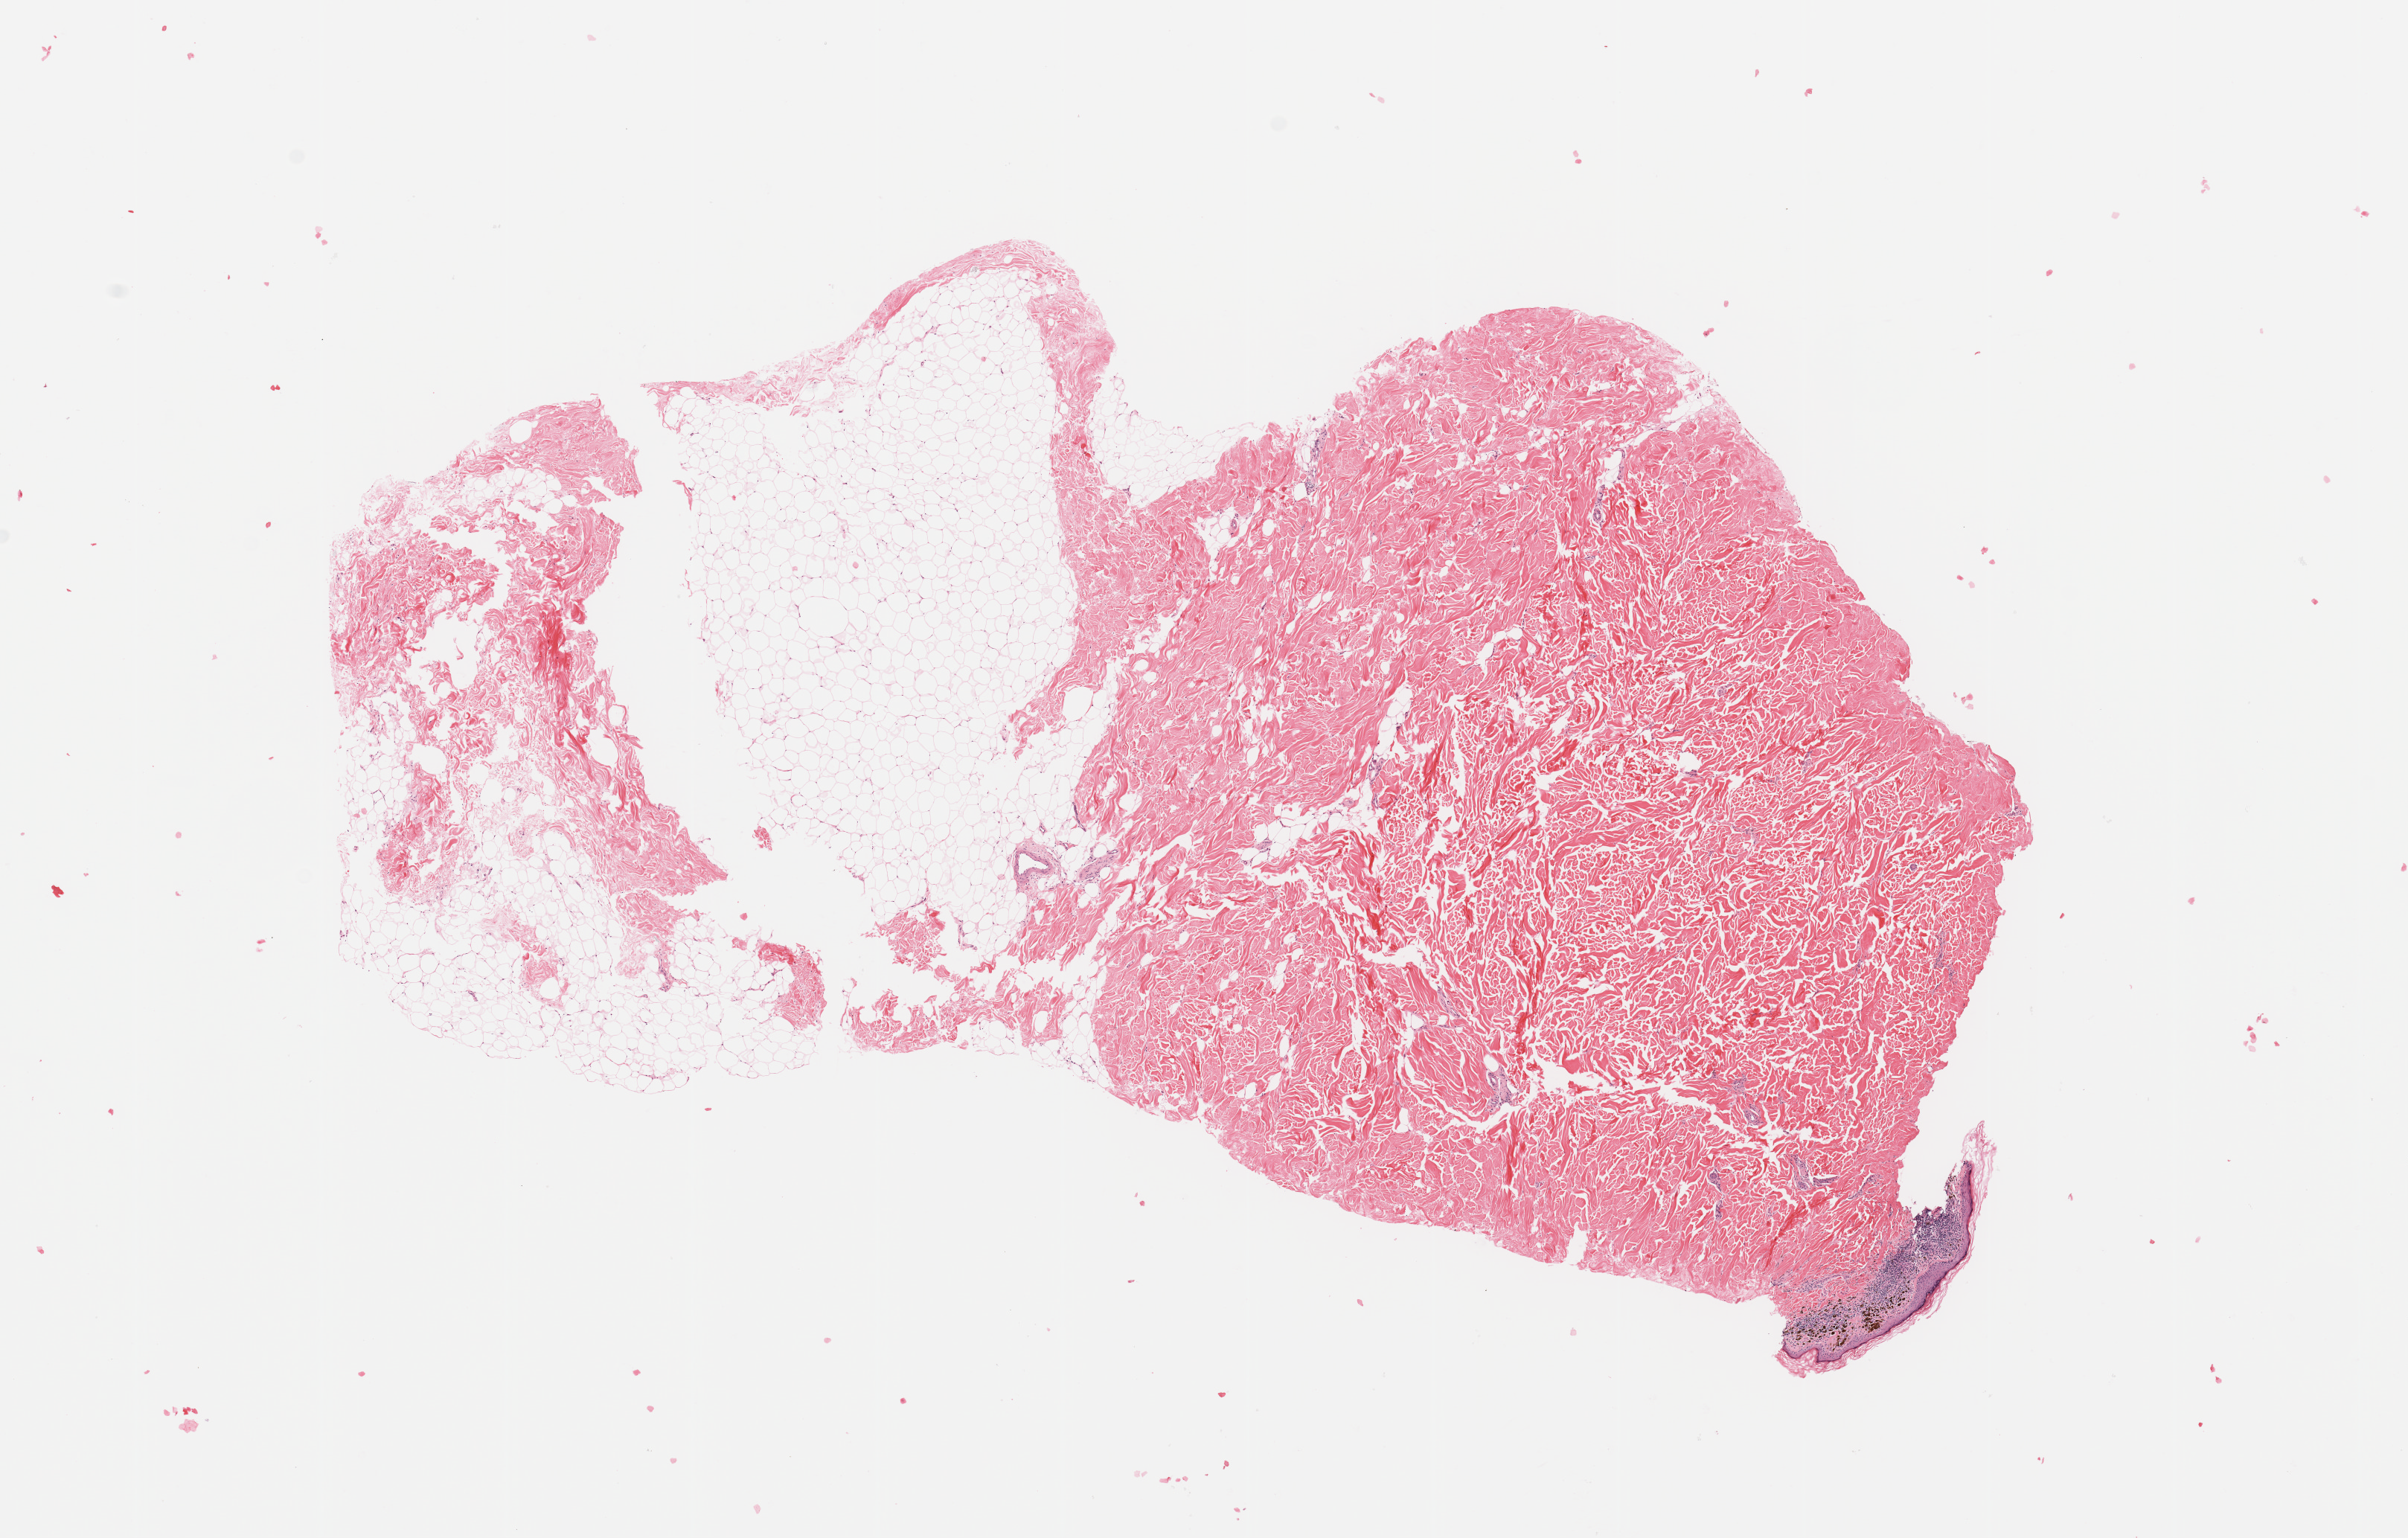
Whole-slide histology image, H&E-stained, low-resolution overview of the scanned area, about 12.8 x 8.2 mm (from a 20x scan); melanoma tumour tissue; sampled site not recorded. Patient: female, age 66 years.
Patient diagnosis (cohort enrolment): cutaneous melanoma (skin). Primary tumour site (as recorded): head & neck.